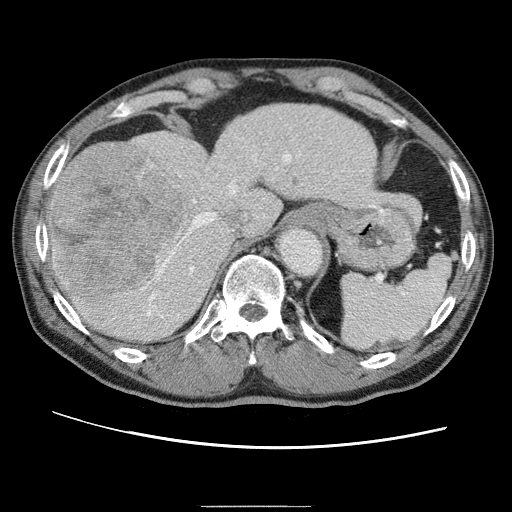
Contrast-enhanced abdominal CT (liver protocol), one axial slice; position 45 of 75 along the scan axis; reconstruction kernel STANDARD; one of 2 acquisitions stored at this slice position; soft-tissue window (W 400 / L 40 HU); 512 × 512 image matrix, field of view 360 × 360 mm. From the clinical record (not read from this slice): diagnosis: hepatocellular carcinoma (patient treated with transarterial chemoembolisation; whether this scan precedes or follows treatment is not stated here); TNM stage (as recorded): Stage-II.
Structures marked on this image (semi-automatic segmentation, software-assisted and operator-edited):
- abdominal aorta: box from (x=278, y=230) to (x=322, y=276) px
- liver parenchyma outside the tumour (the mass and vessels are separate outlines, so this box may not span the whole liver): (x=48, y=104)–(x=382, y=342)
- mass: (x=49, y=147)–(x=186, y=298)
- liver vessels: (x=151, y=154)–(x=306, y=307)